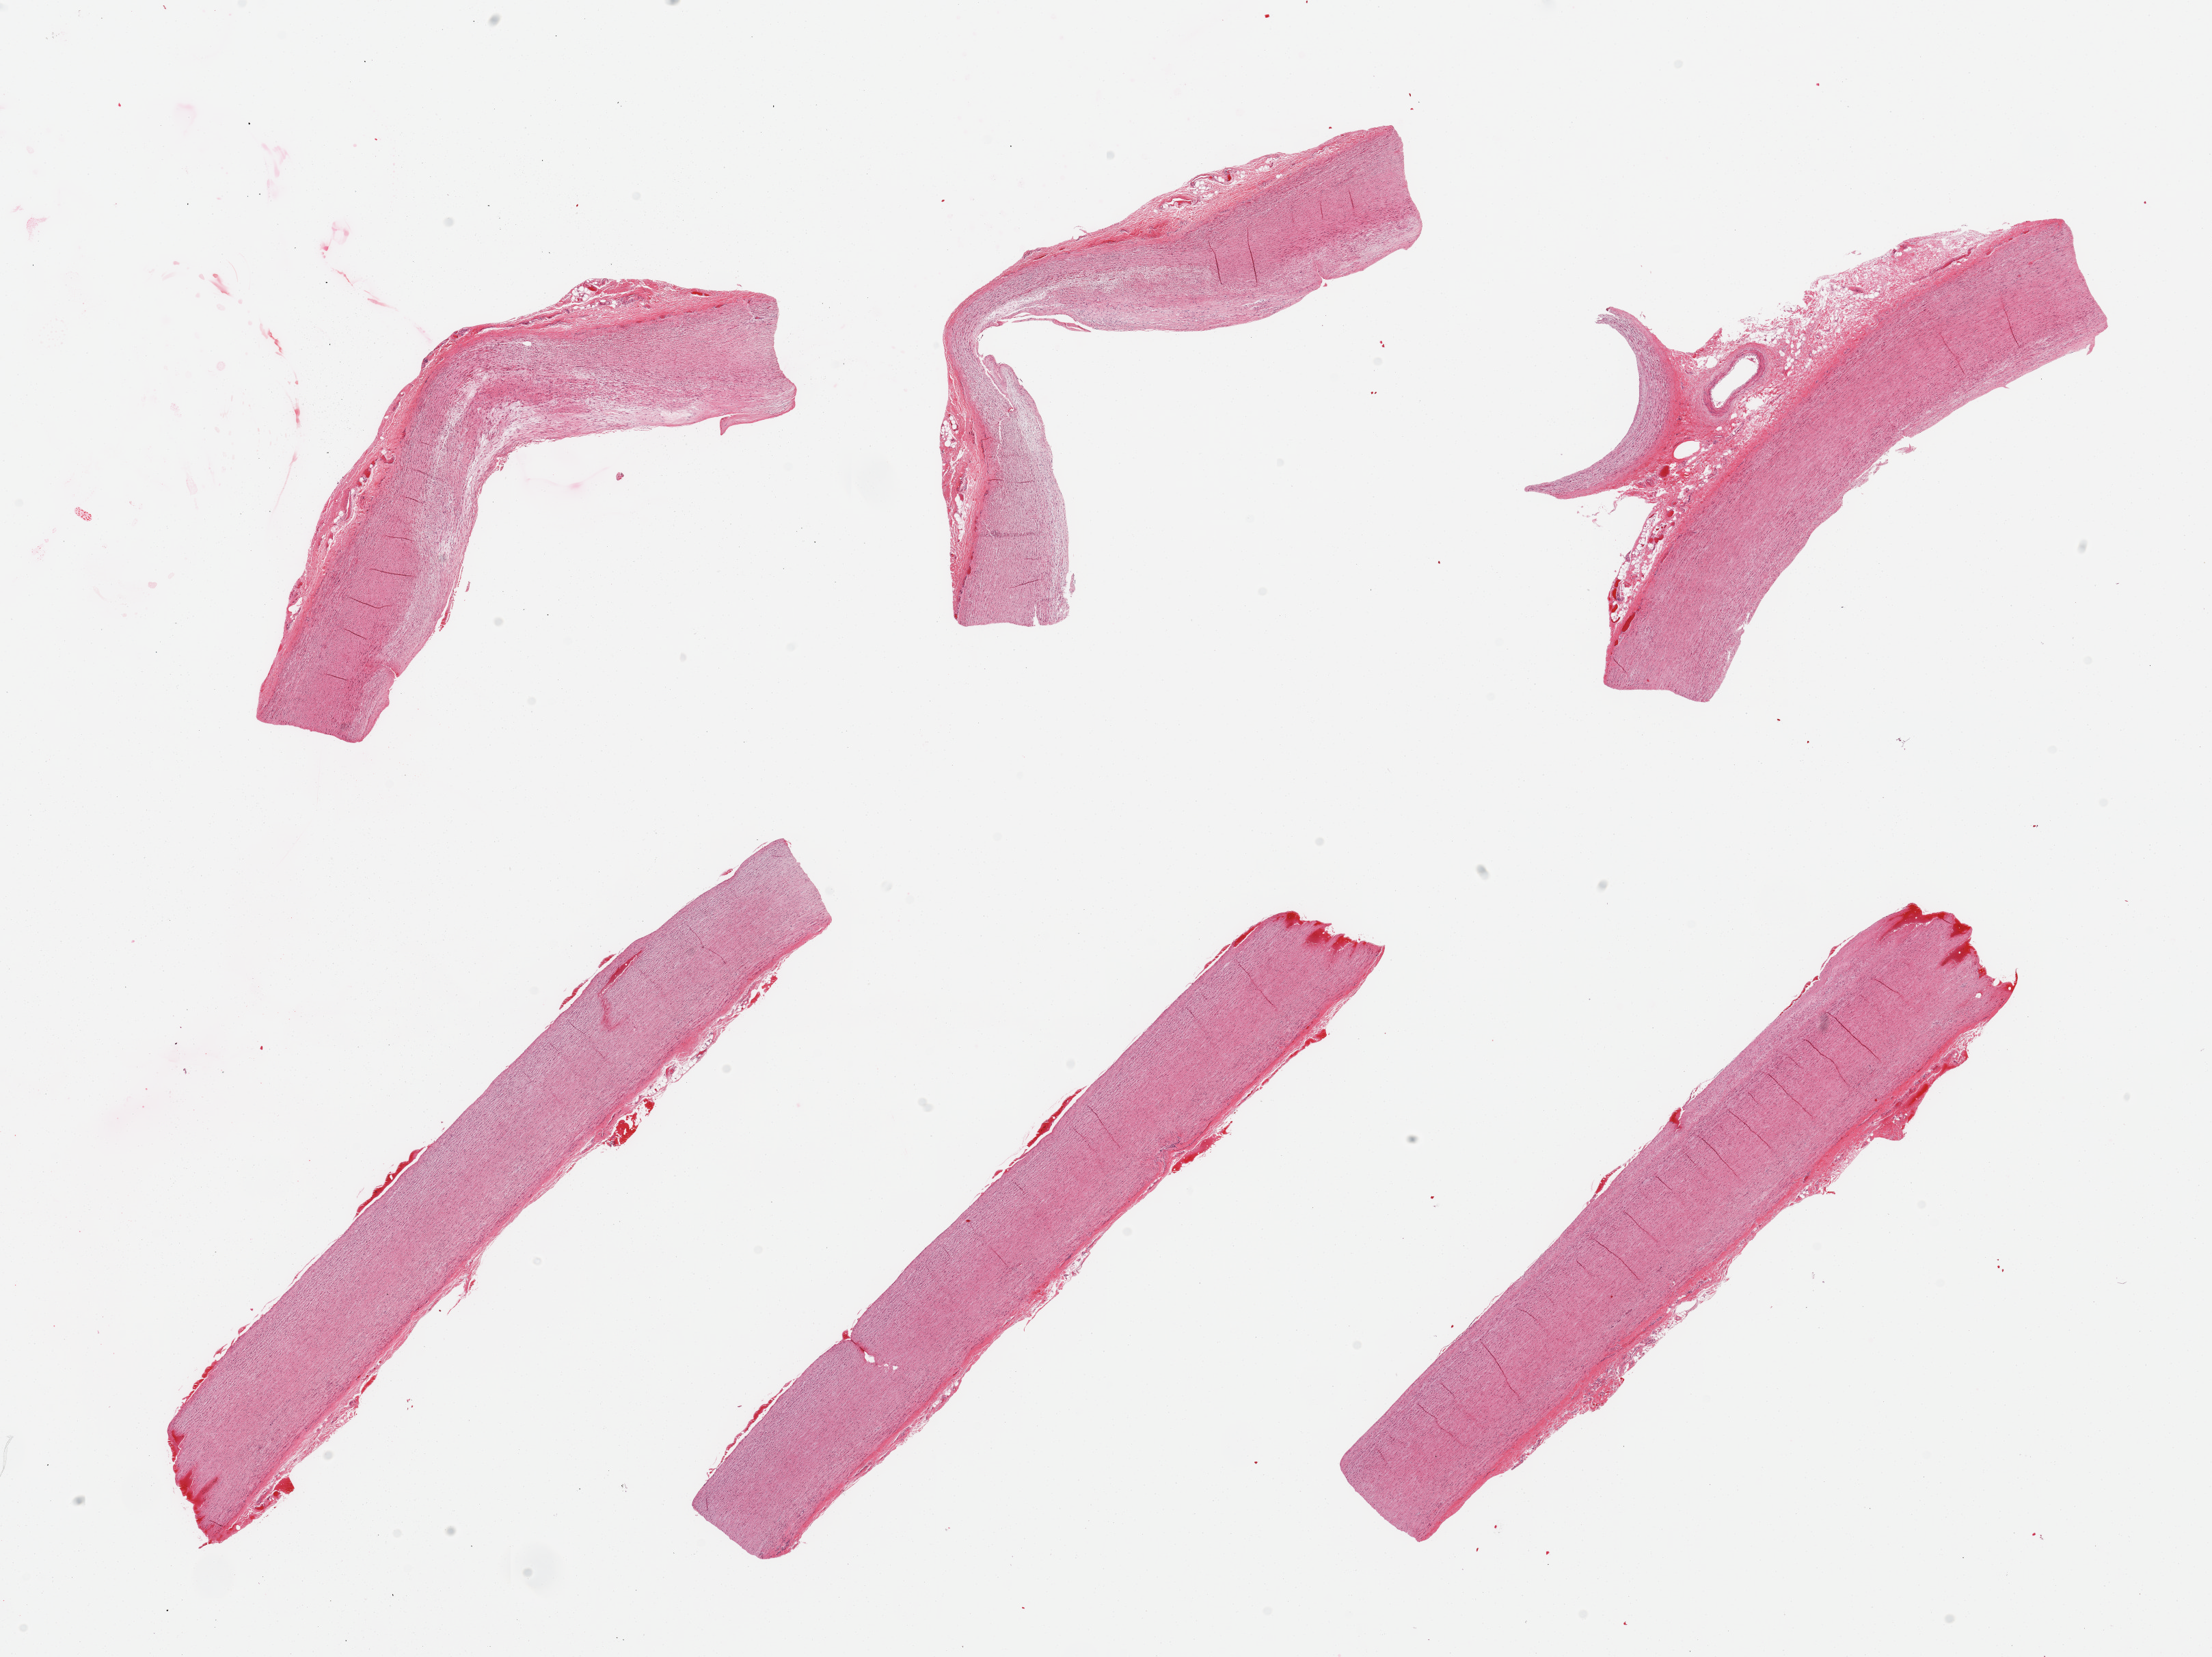
Whole-slide image, hematoxylin and eosin (H&E) stain — shown as a low-resolution overview of the whole scanned area (about 25.6 x 19.2 mm), PAXgene-fixed paraffin-embedded (PFPE) section, target tissue: aorta, donor tissue sample. Donor: female.
Reviewer comment on this tissue sample: 6 pieces, mild atherosis.